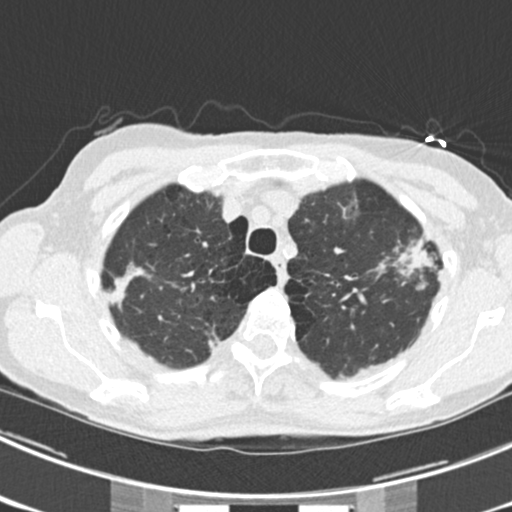
Axial slice from a low-dose chest CT screening exam. Third annual screen. Lung window (W 1500 / L -600 HU). 2 mm slice thickness. Standard (soft-tissue) reconstruction kernel (B30f). 120 kVp. Female, age 63 years at enrolment. Current smoker at enrolment.
• Lesion marked by an expert reader, bounding box [x1, y1, x2, y2] px = [376, 228, 447, 289].
• The screening reader recorded 9 non-calcified nodules or masses ≥4 mm on this exam (left upper lobe, right upper lobe, left upper lobe, left lower lobe, right middle lobe, left lower lobe, left lower lobe, right lower lobe, right lower lobe); which of them this box marks is not recorded.
• Later outcome: lung cancer diagnosed 15 days after this screen — bronchiolo-alveolar adenocarcinoma, NOS, right upper lobe, right middle lobe, right lower lobe, left upper lobe, left lower lobe, moderately differentiated (G2), stage IV (AJCC 6th edition).